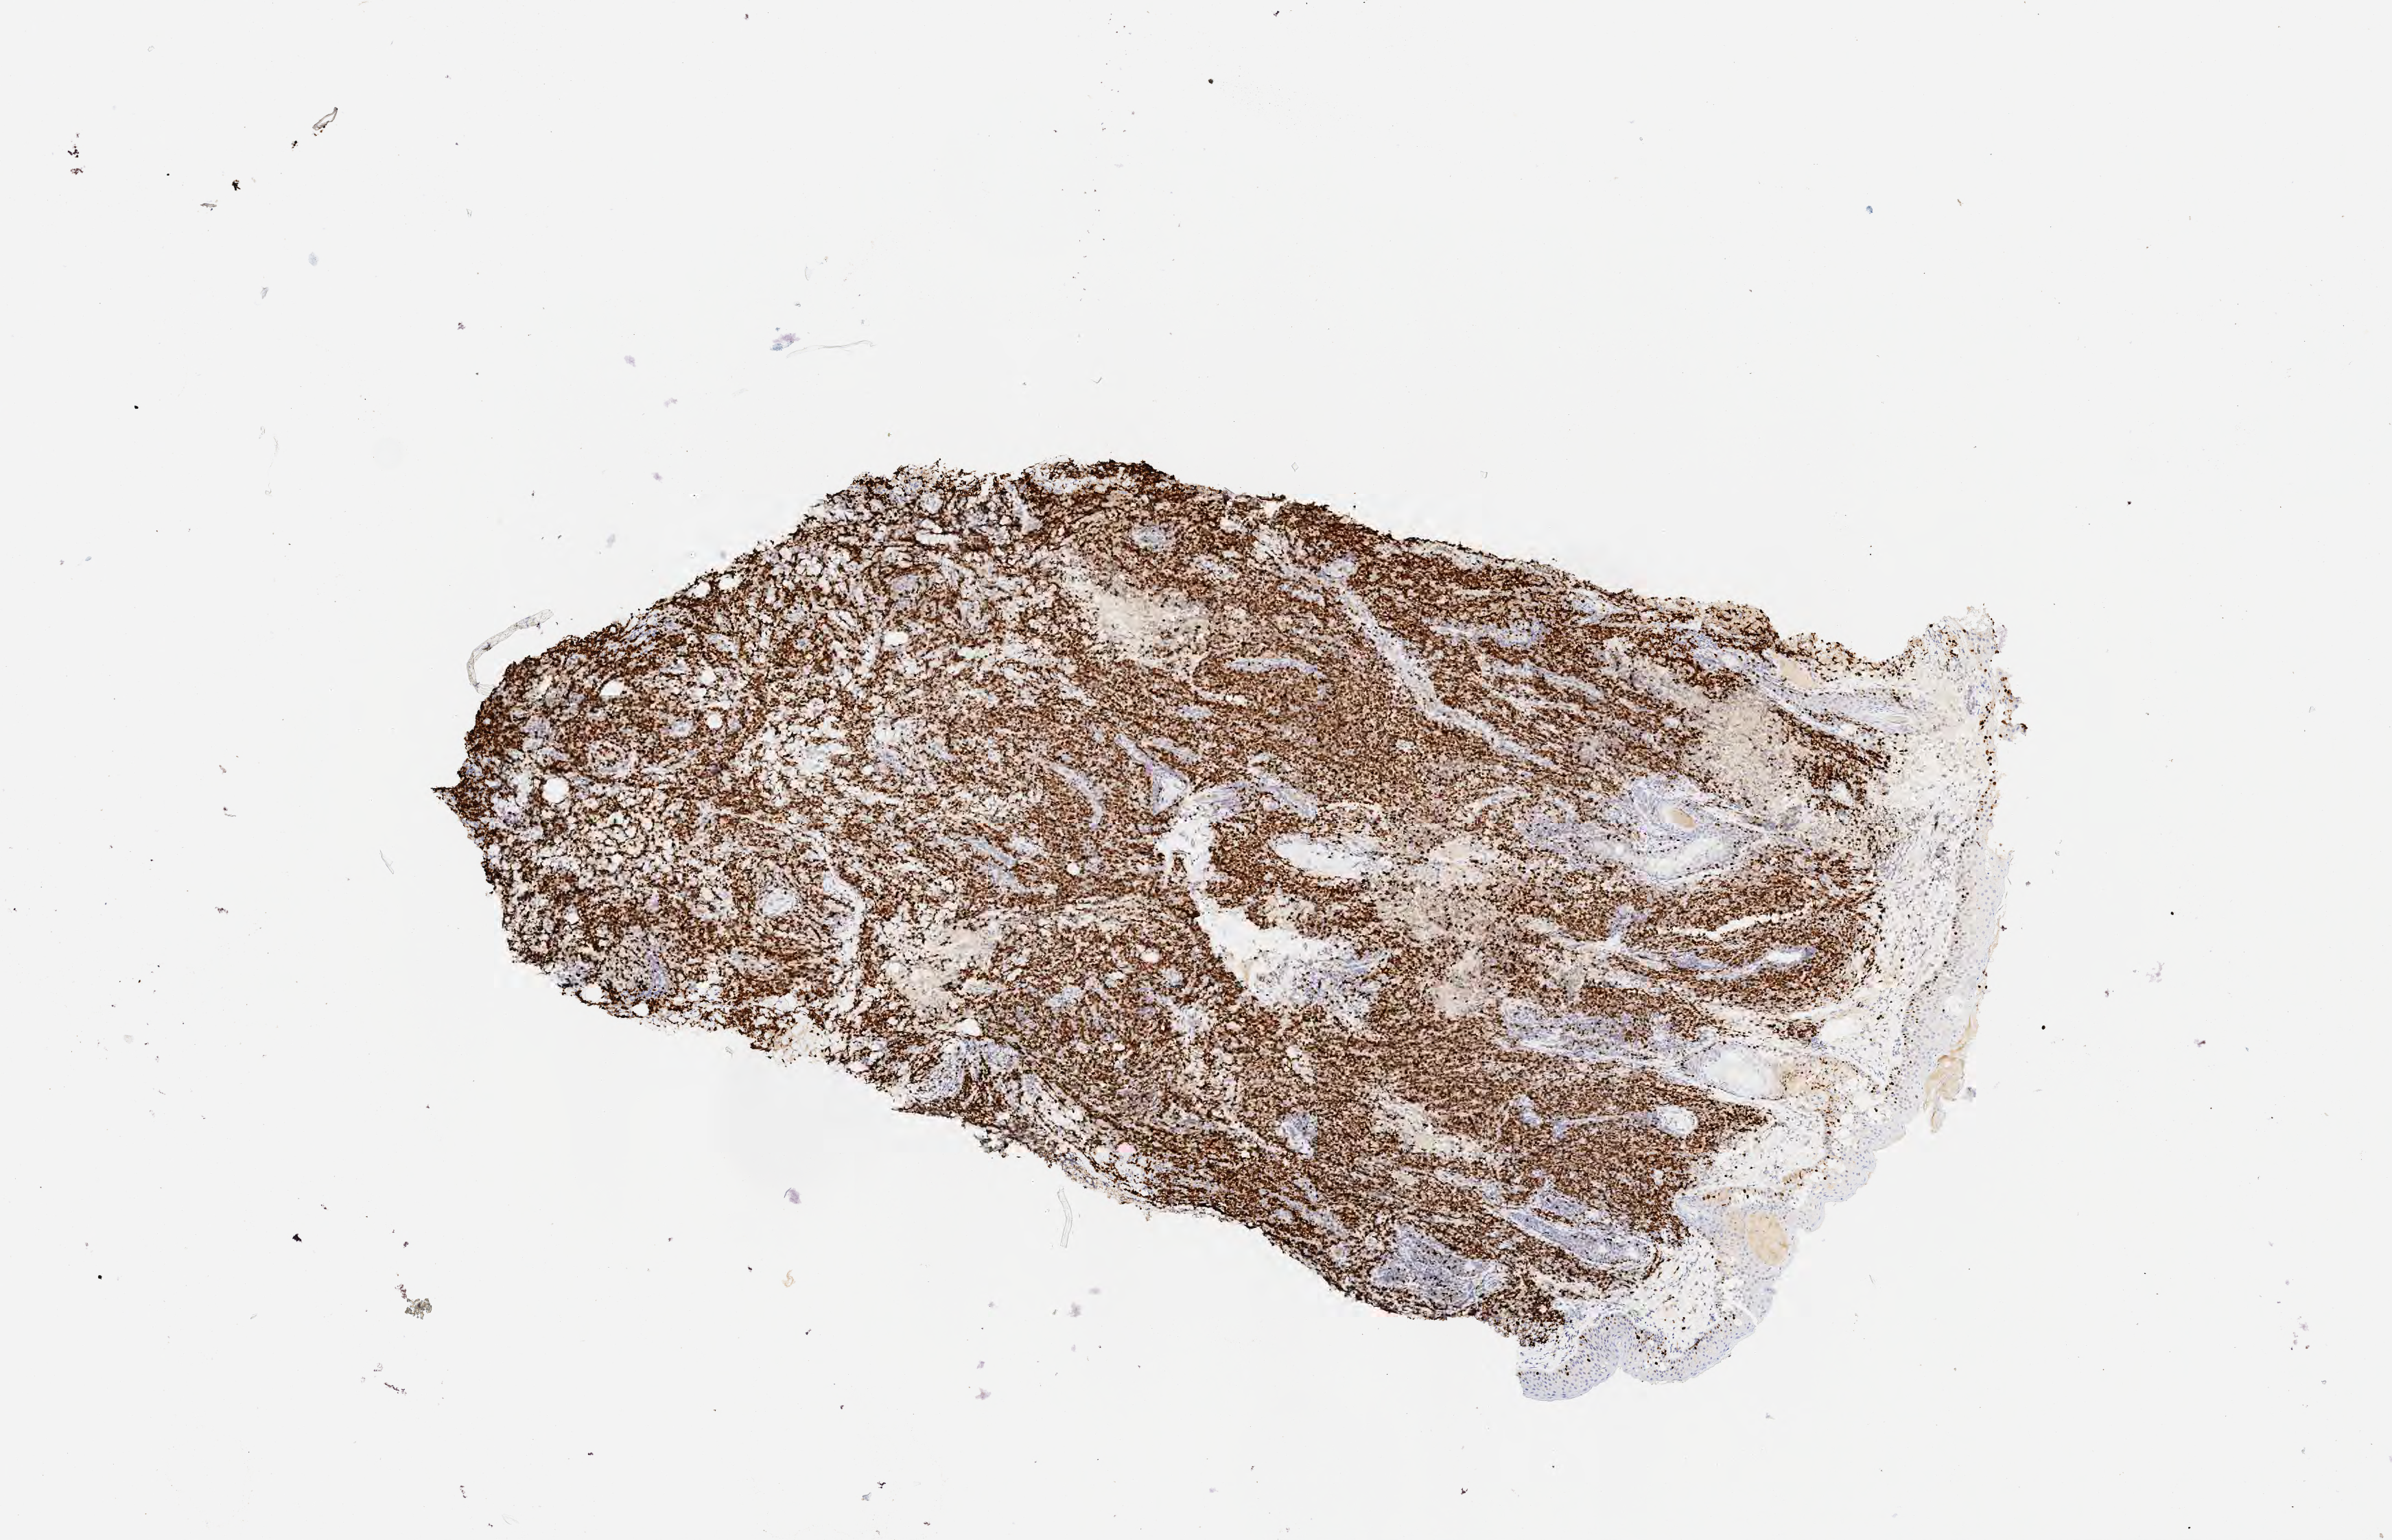
Immunohistochemistry (IHC) whole-slide image stained for Ki-67 — shown as a low-resolution overview of the whole scanned area (about 7.0 x 4.5 mm), tumor tissue. Male patient, 41 years old.
Histologic diagnosis: Diffuse large B-cell lymphoma, NOS.